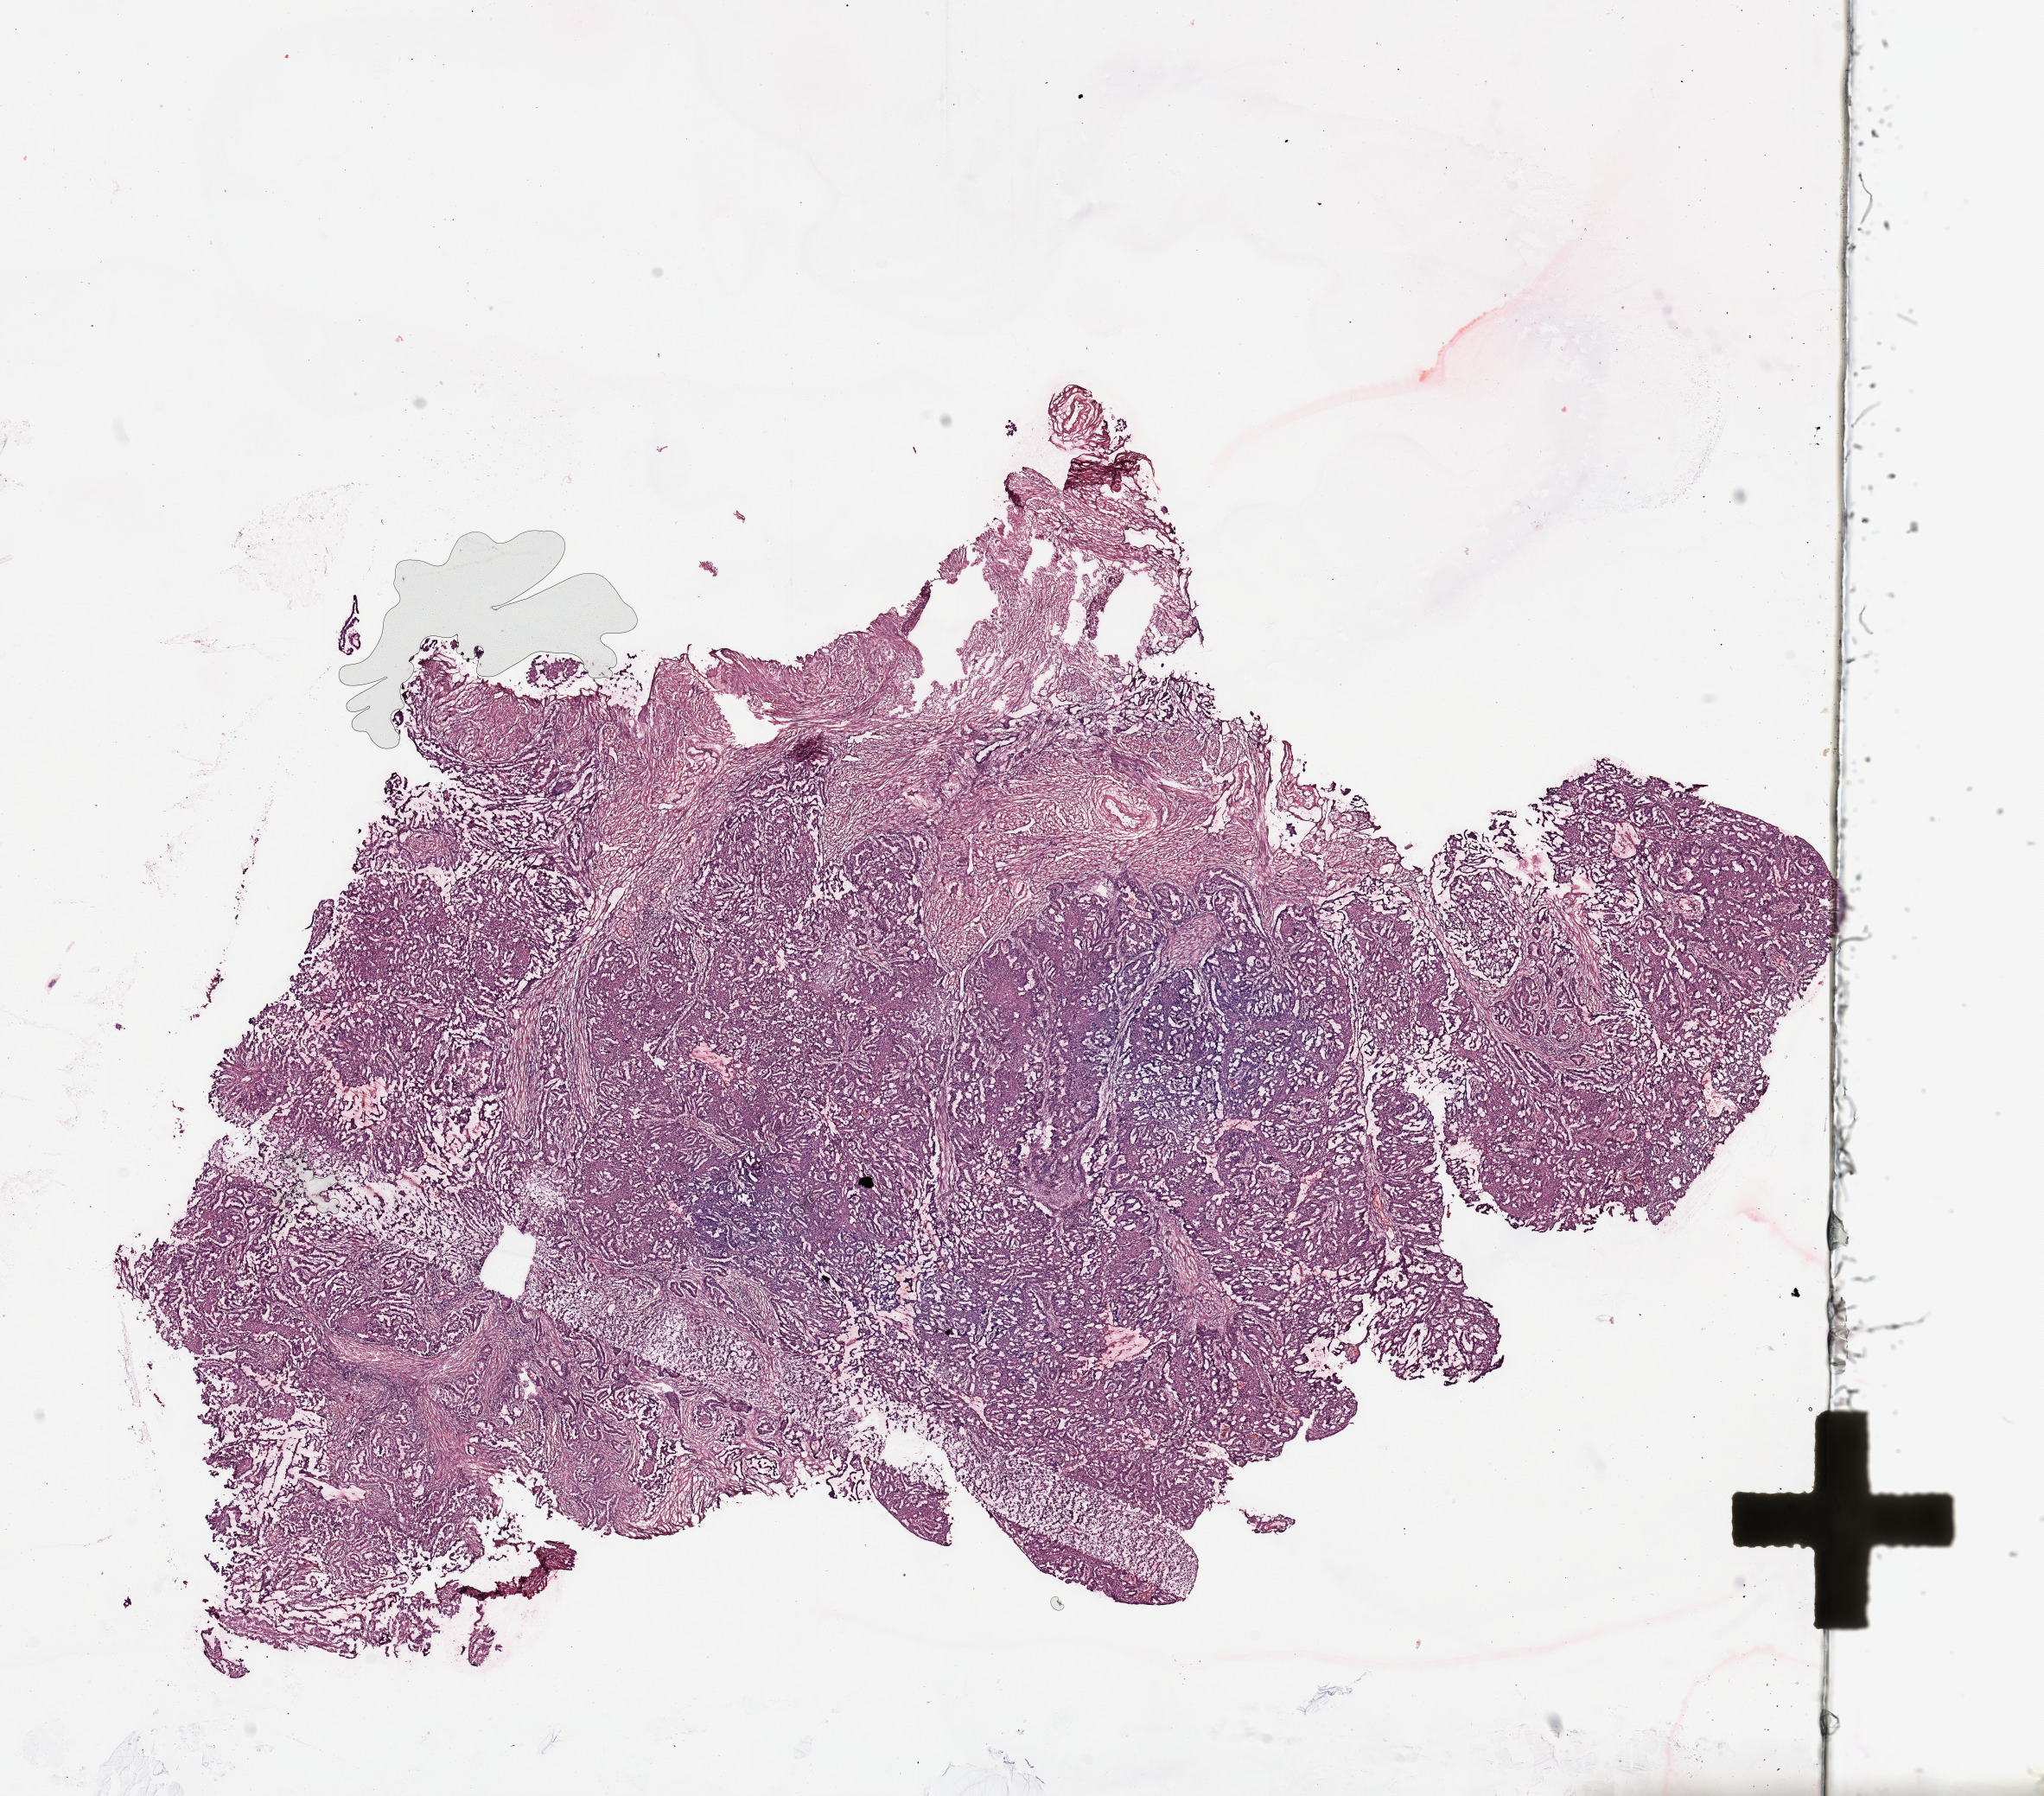
Whole-slide histology image, H&E — shown as a low-resolution overview of the whole scanned area (about 18.7 x 16.4 mm, from a 20x scan); tumour tissue sample, uterus. Female, 44 y/o. Histologic grade: G1 (well differentiated).
AJCC pathologic stage: I. Histologic diagnosis: Endometrioid adenocarcinoma, NOS.